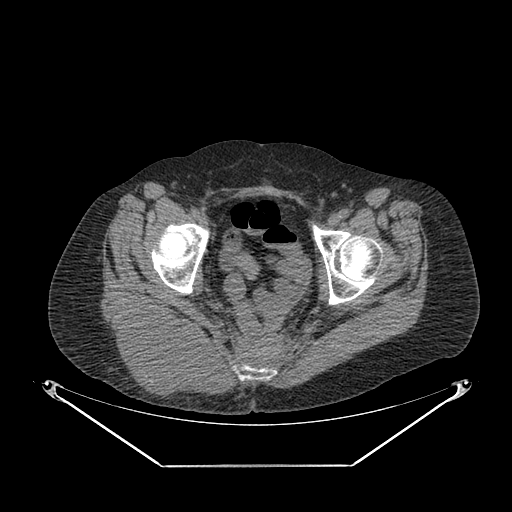
CT of an extremity soft-tissue mass (from a PET/CT study), one axial slice; position 57 of 267 along the scan axis; reconstruction kernel SOFT; 140 kVp; soft-tissue window (W 400 / L 40 HU); 512 × 512 image matrix, field of view 500 × 500 mm. Female patient. Case-level facts recorded for this patient, not image findings: histological type: spindle cell suggestive of myxofibrosarcoma; grade: intermediate; site of the primary tumour: right buttock.
Outlined on this slice (expert contour drawn on MRI and transferred to this co-registered scan by the dataset authors):
- gross tumour volume (mass): bounding box <109,304,220,403> (left, top, right, bottom; pixels)